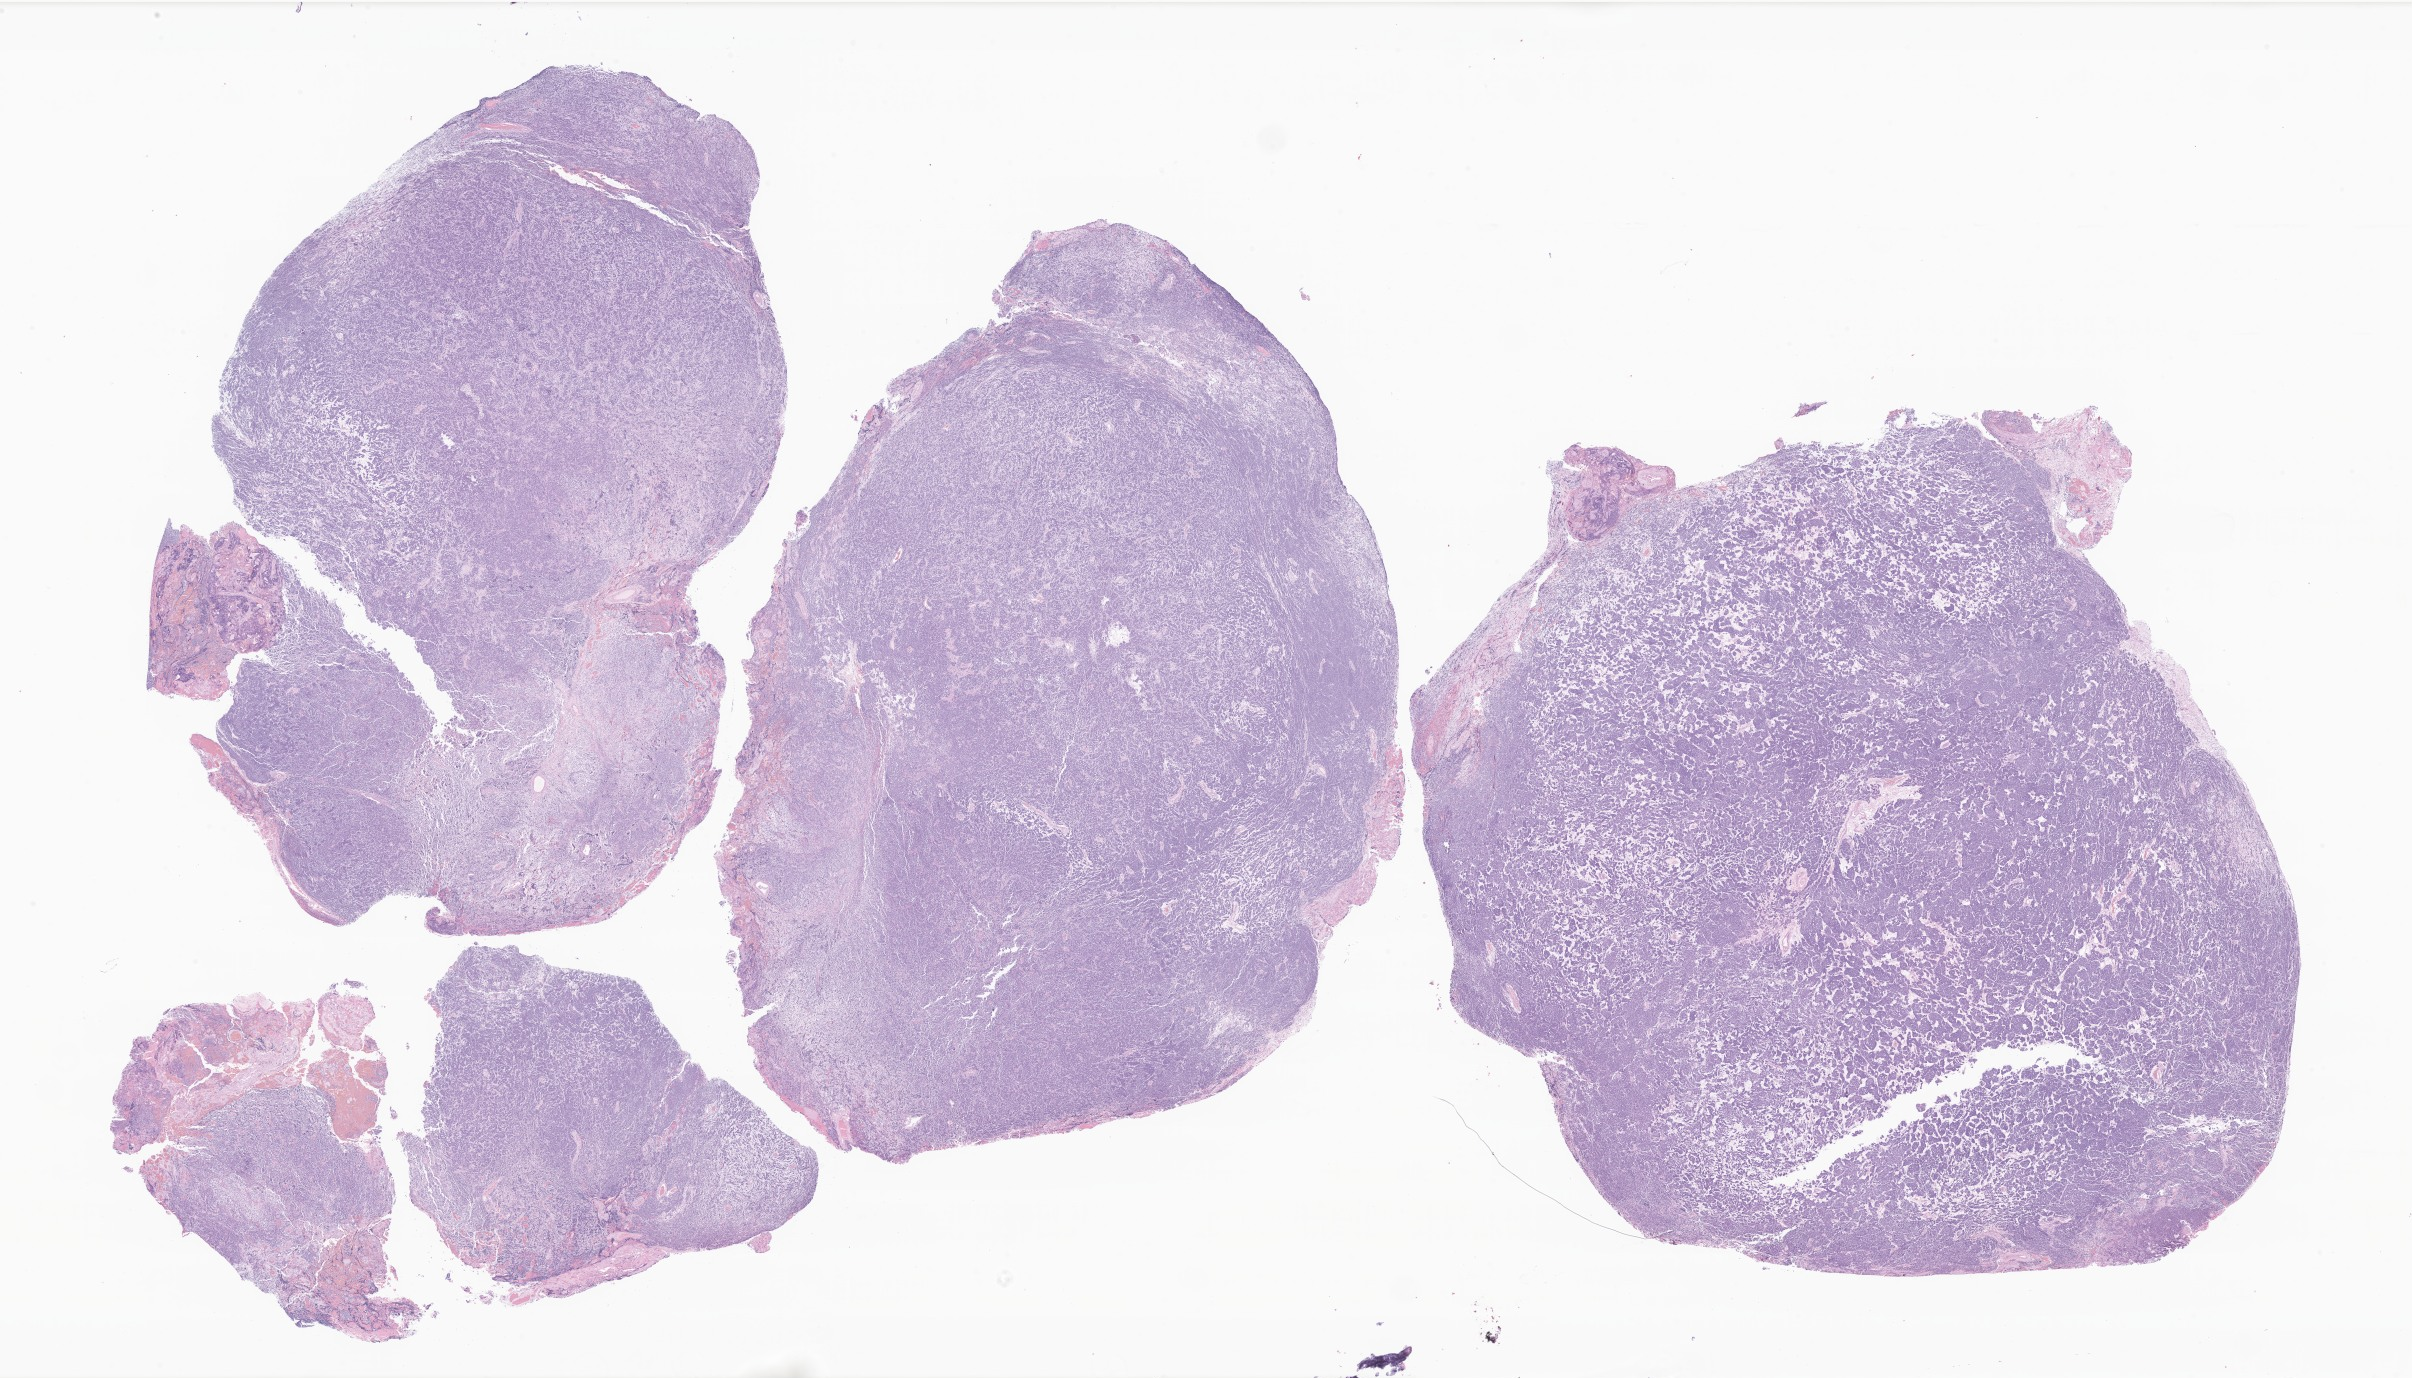
Whole-slide image, H&E stain of tumor tissue from the cerebellum — low-resolution overview of the scanned area, about 40.7 x 23.2 mm, FFPE section. Patient male; age 140 months (11 years 8 months).
Recorded diagnosis: Medulloblastoma, NOS.